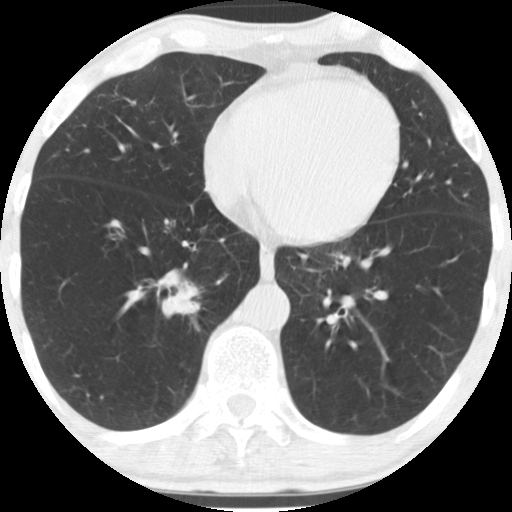
Low-dose screening chest CT, axial slice; baseline screening round; lung window (W 1500 / L -600 HU); 2.5 mm slice thickness; standard (soft-tissue) reconstruction kernel (STANDARD); slice 115 of 170 in the series; 512 × 512 image matrix, field of view 290 × 290 mm. Male participant, aged 67 years at enrolment.
- Expert reader's lesion annotation, bounding box [x1, y1, x2, y2] px = [155, 273, 218, 330].
- Reader record for this screening exam (exam-level; its link to the box is not recorded): non-calcified nodule or mass ≥4 mm, right lower lobe, 16 × 16 mm, spiculated (stellate) margins, soft tissue attenuation.
- Later outcome: lung cancer diagnosed 49 days after this screen — squamous cell carcinoma, NOS, right lower lobe, moderately differentiated (G2), stage IA (AJCC 6th edition), 20 mm at pathology.